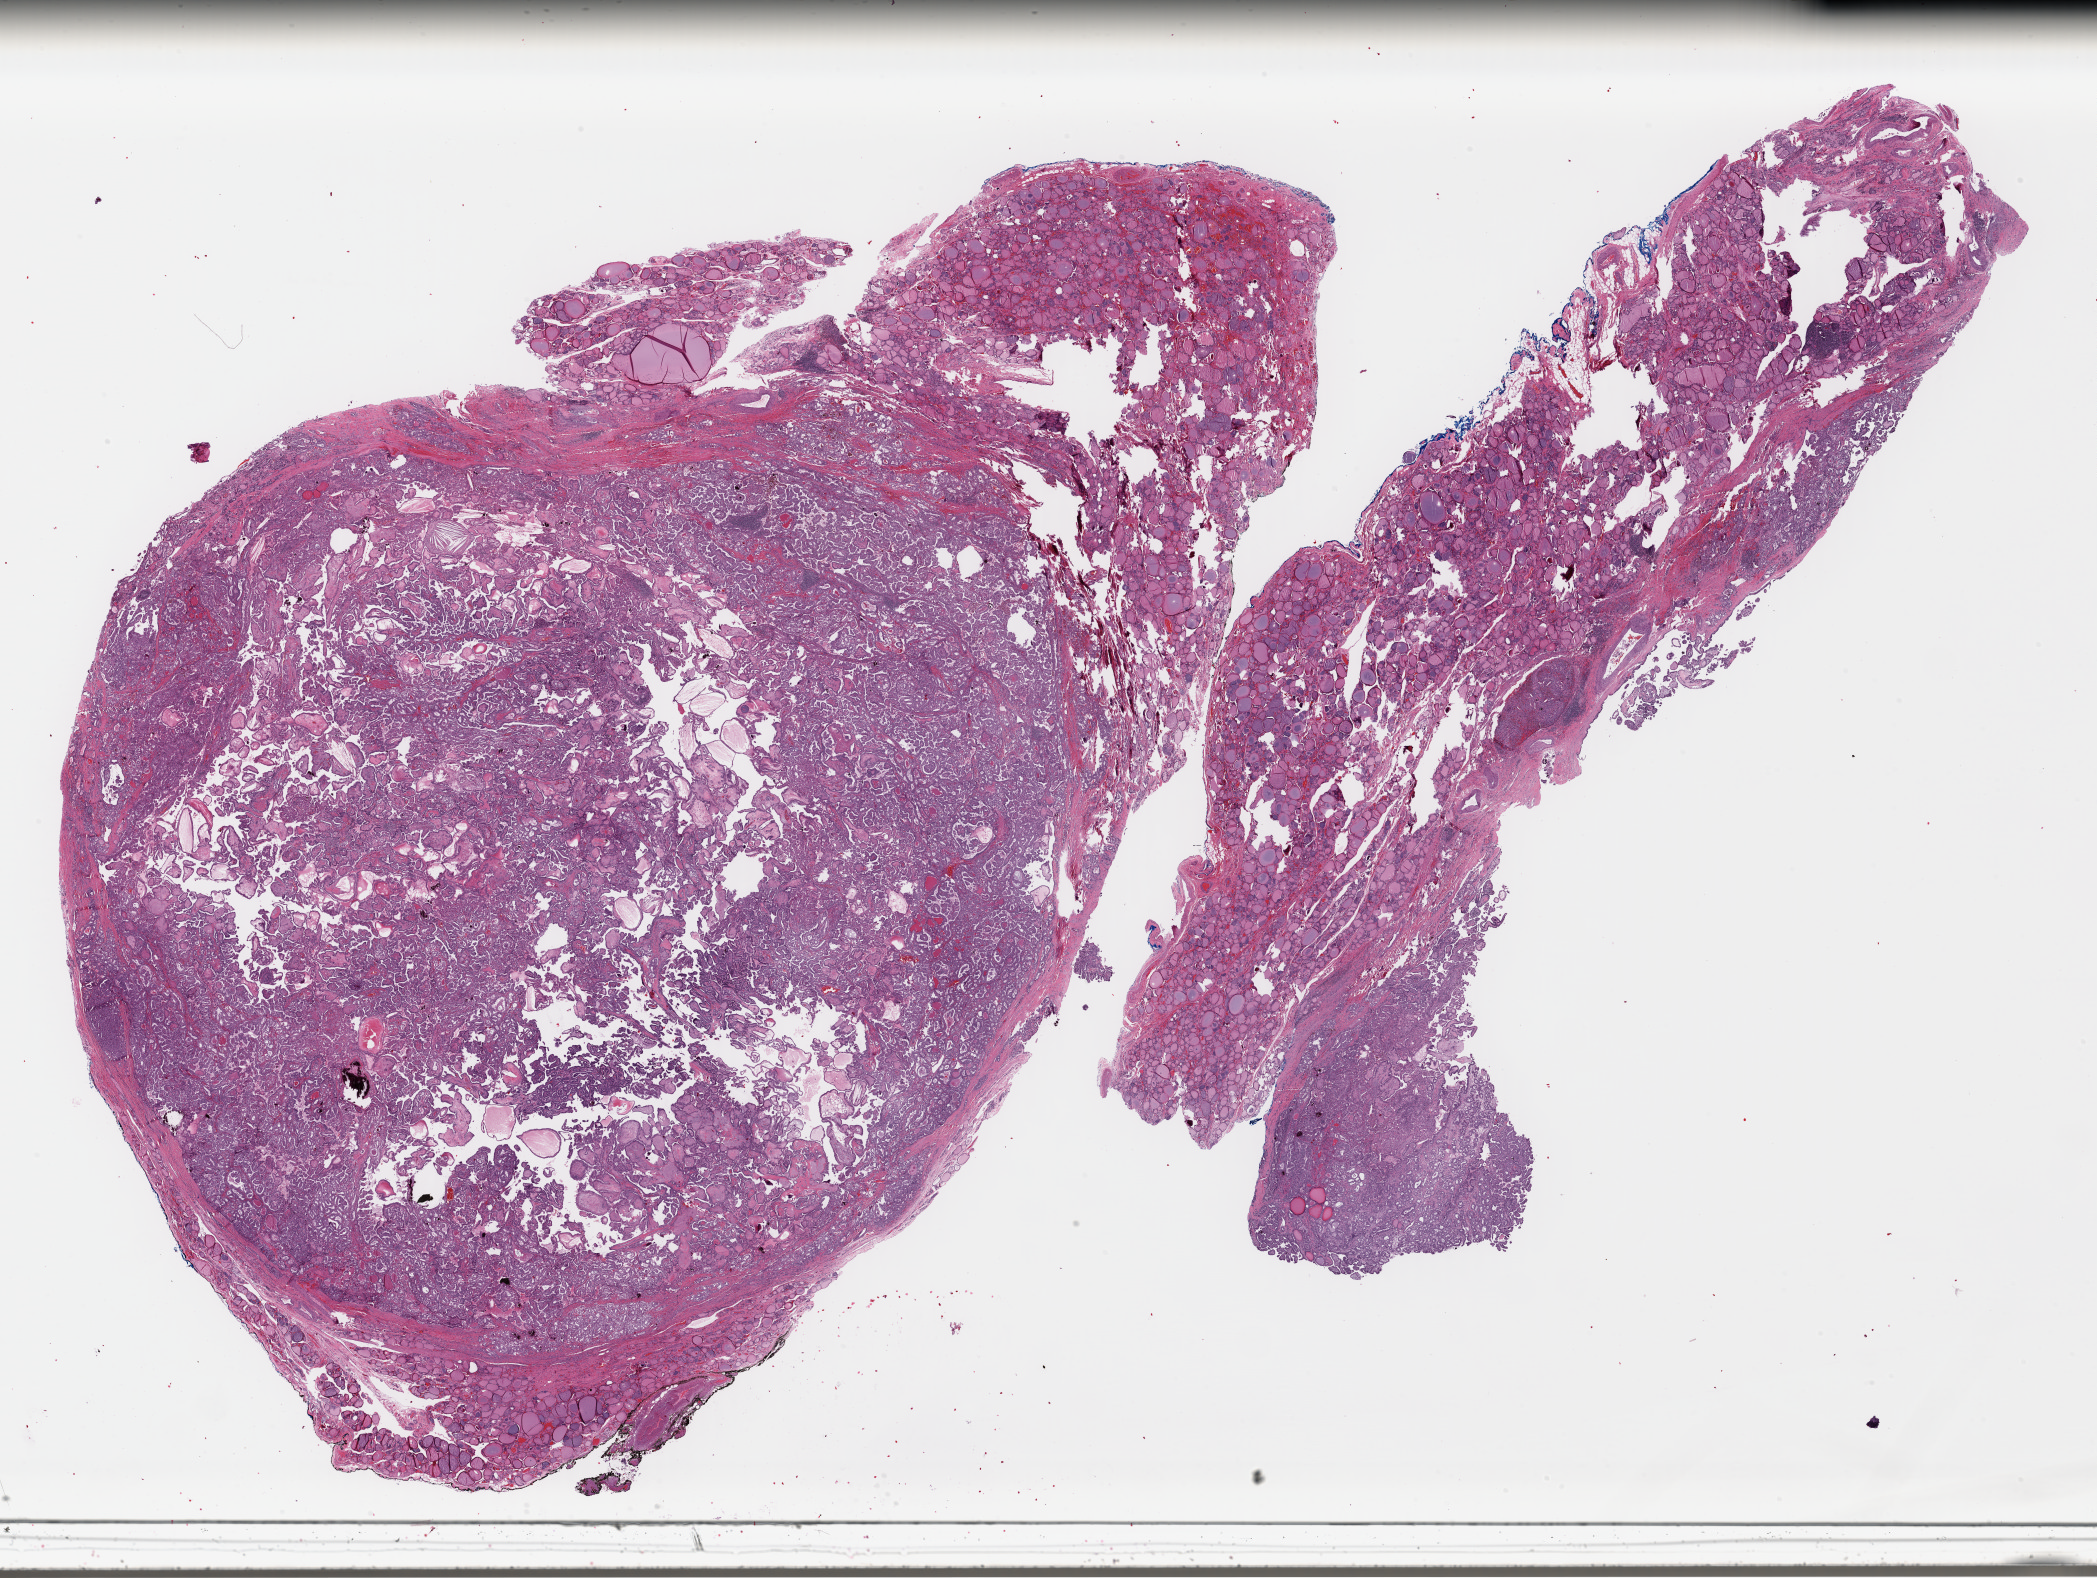
Digitized H&E tissue section (whole slide) — low-resolution overview of the scanned area, about 33.0 x 24.8 mm (from a 40x scan); formalin-fixed paraffin-embedded (FFPE) diagnostic section; thyroid, primary tumour sample. Male, age 65 years at initial diagnosis.
TNM: T3 N1a M0. Diagnosis: Papillary adenocarcinoma, NOS (thyroid gland). Lymph nodes positive (case pathology): 1 of 1 examined. AJCC pathologic stage: III.